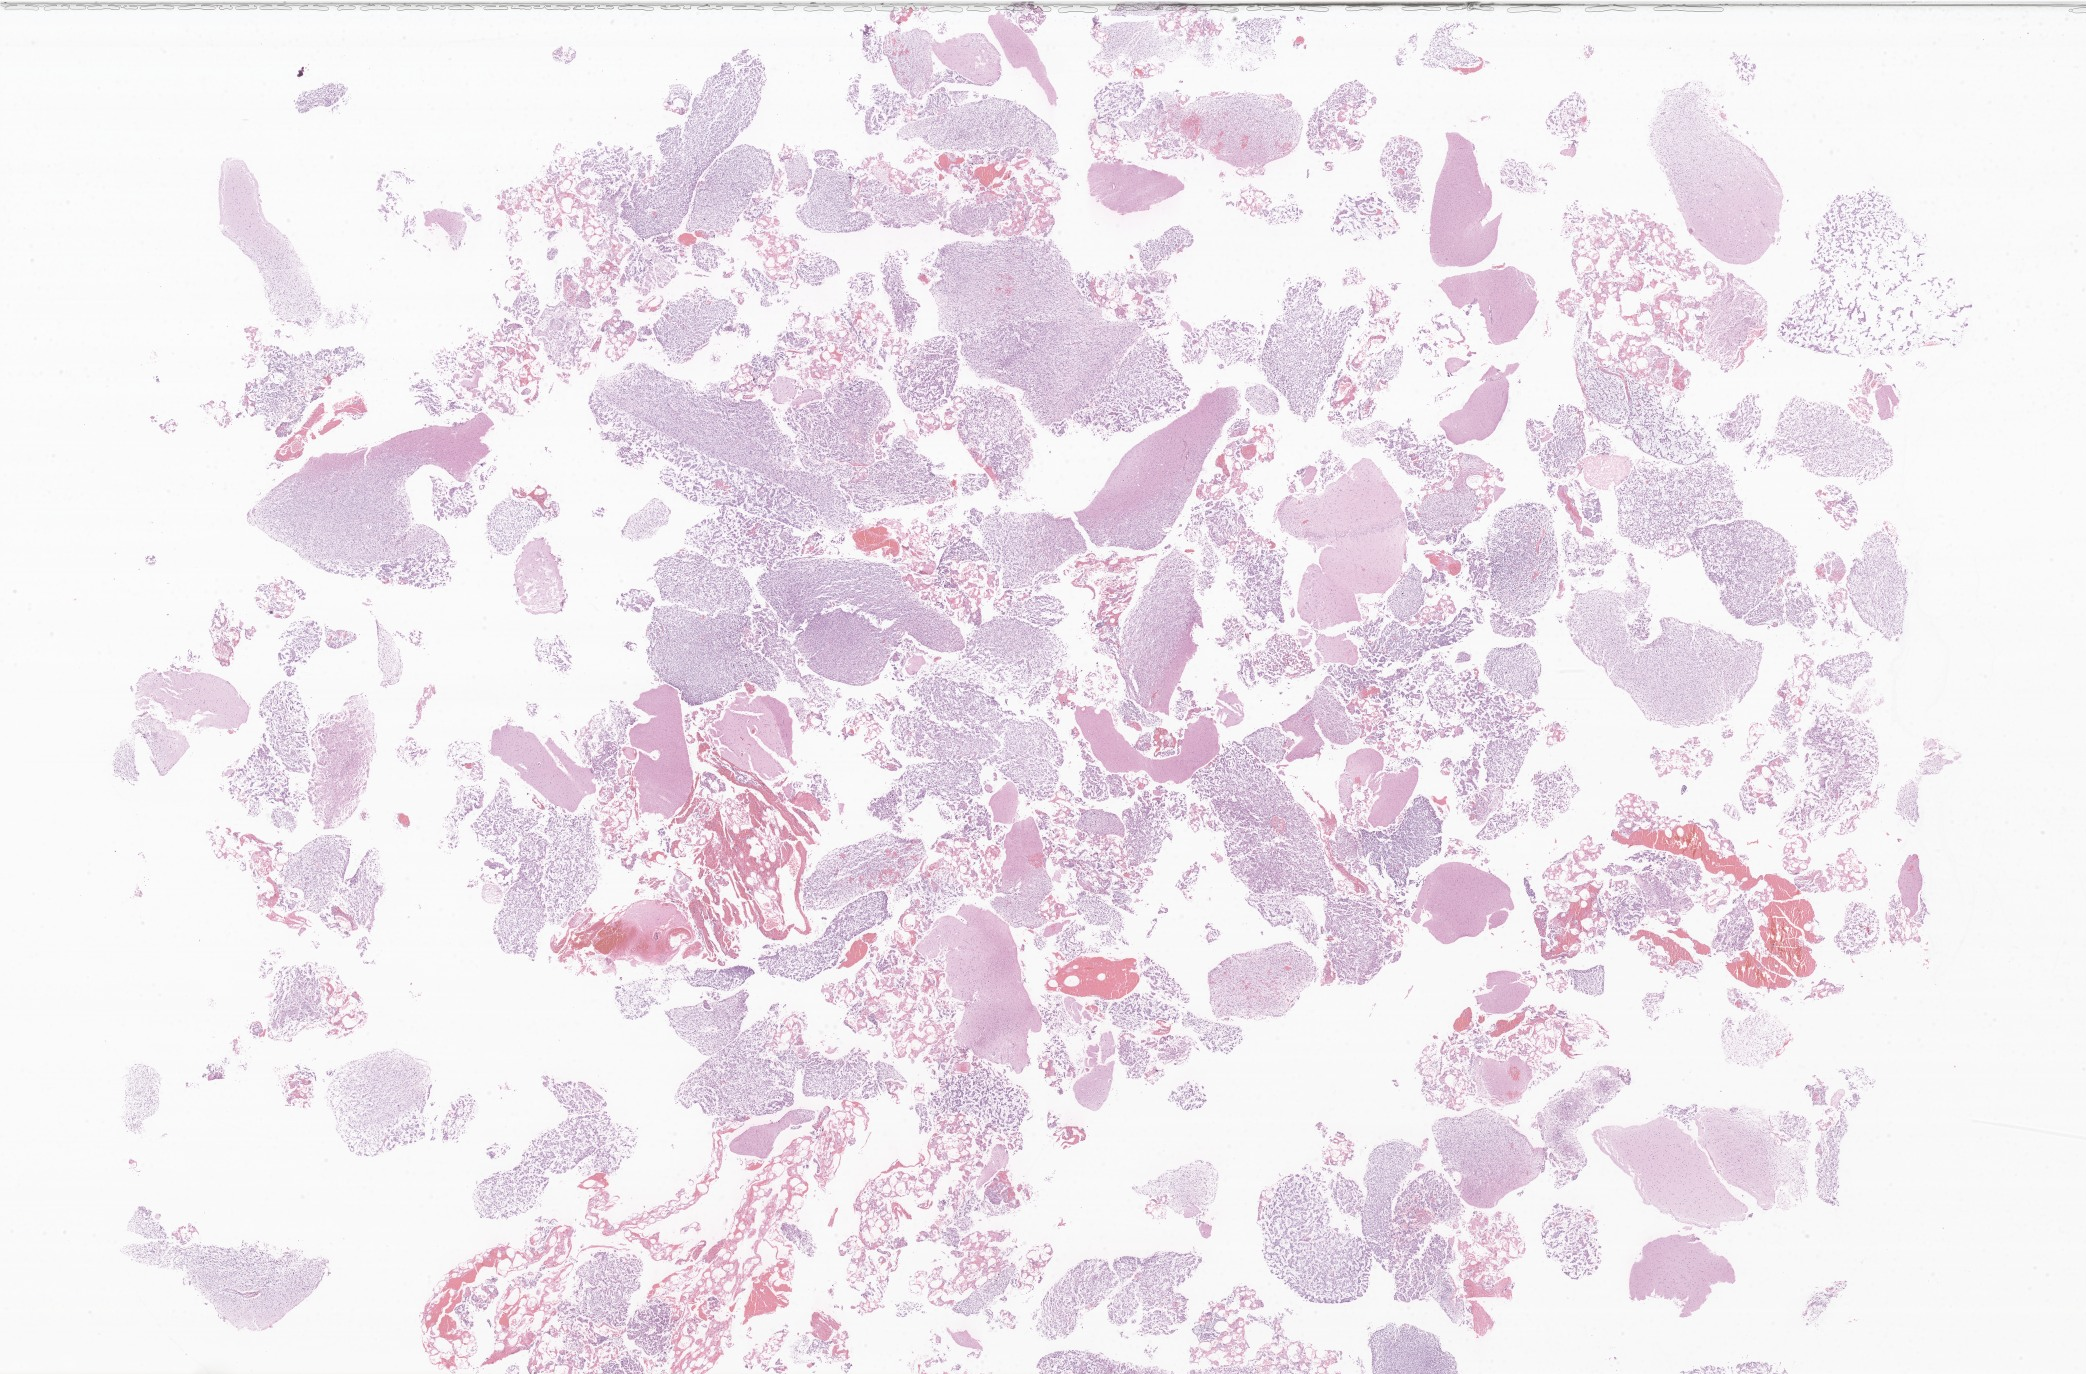
Digitized haematoxylin and eosin-stained section of tumor tissue from the temporal lobe — whole scanned area (about 35.2 x 23.2 mm) shown as a low-resolution overview. Formalin-fixed, paraffin-embedded (FFPE) tissue. Female patient, age 221 months (18 years 5 months).
Diagnosis: Glioma, malignant.